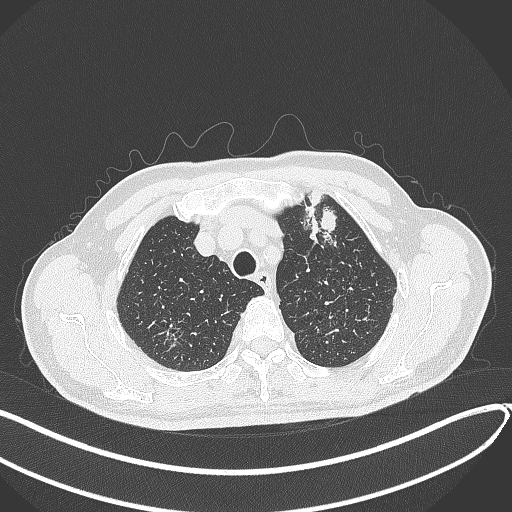
Chest CT, one axial slice; slice 350 of 459 in the series (ordered by position); reconstruction kernel B70f; lung window (W 1500 / L -600 HU); 512 × 512 image matrix, field of view 400 × 400 mm. Male patient, age 74 years. From the clinical record (not read from this slice): clinical TNM (as recorded): T2b N0 M1c.
Structures marked on this image (rectangle marked by the reading radiologist):
- lung tumour (recorded histology: adenocarcinoma): bounding box <301,185,344,248> (left, top, right, bottom; pixels)